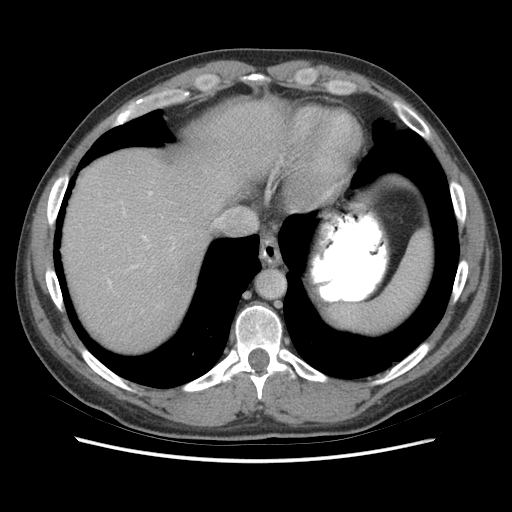
Contrast-enhanced abdominal CT (liver protocol), one axial slice. Reconstruction kernel STANDARD. Soft-tissue window (W 400 / L 40 HU). 2.5 mm slice thickness. 512 × 512 image matrix, field of view 360 × 360 mm. Case-level facts recorded for this patient, not image findings: diagnosis: hepatocellular carcinoma (patient treated with transarterial chemoembolisation; whether this scan precedes or follows treatment is not stated here); TNM stage (as recorded): Stage-IIIA; Child-Pugh class: A; tumour size: 6.6 cm.
Annotated regions visible in this slice (semi-automatic segmentation, software-assisted and operator-edited):
- abdominal aorta: bounding box (x1, y1, x2, y2) in pixels: (257, 270, 285, 298)
- liver parenchyma outside the tumour (the mass and vessels are separate outlines, so this box may not span the whole liver): (62, 100, 286, 352)
- liver vessels: (107, 191, 153, 284)